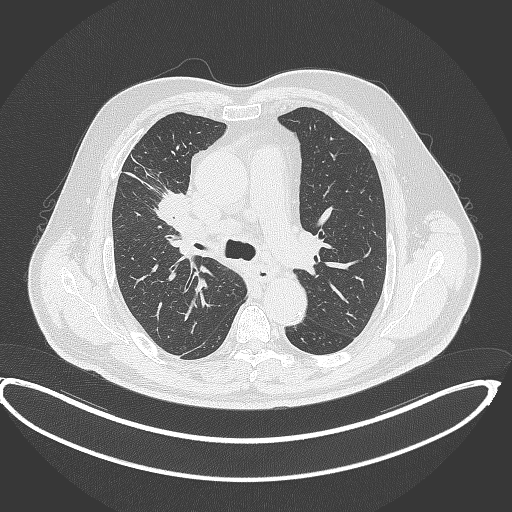
Chest CT, one axial slice. Reconstruction kernel B70f. 120 kVp. Lung window (W 1500 / L -600 HU). 512 × 512 image matrix, field of view 448 × 448 mm. Male patient, age 62 years. From the clinical record (not read from this slice): clinical TNM (as recorded): T1c N3 M1c.
Outlined on this slice (rectangle marked by the reading radiologist):
- lung tumour (recorded histology: adenocarcinoma): bounding box <156,189,197,234> (left, top, right, bottom; pixels)